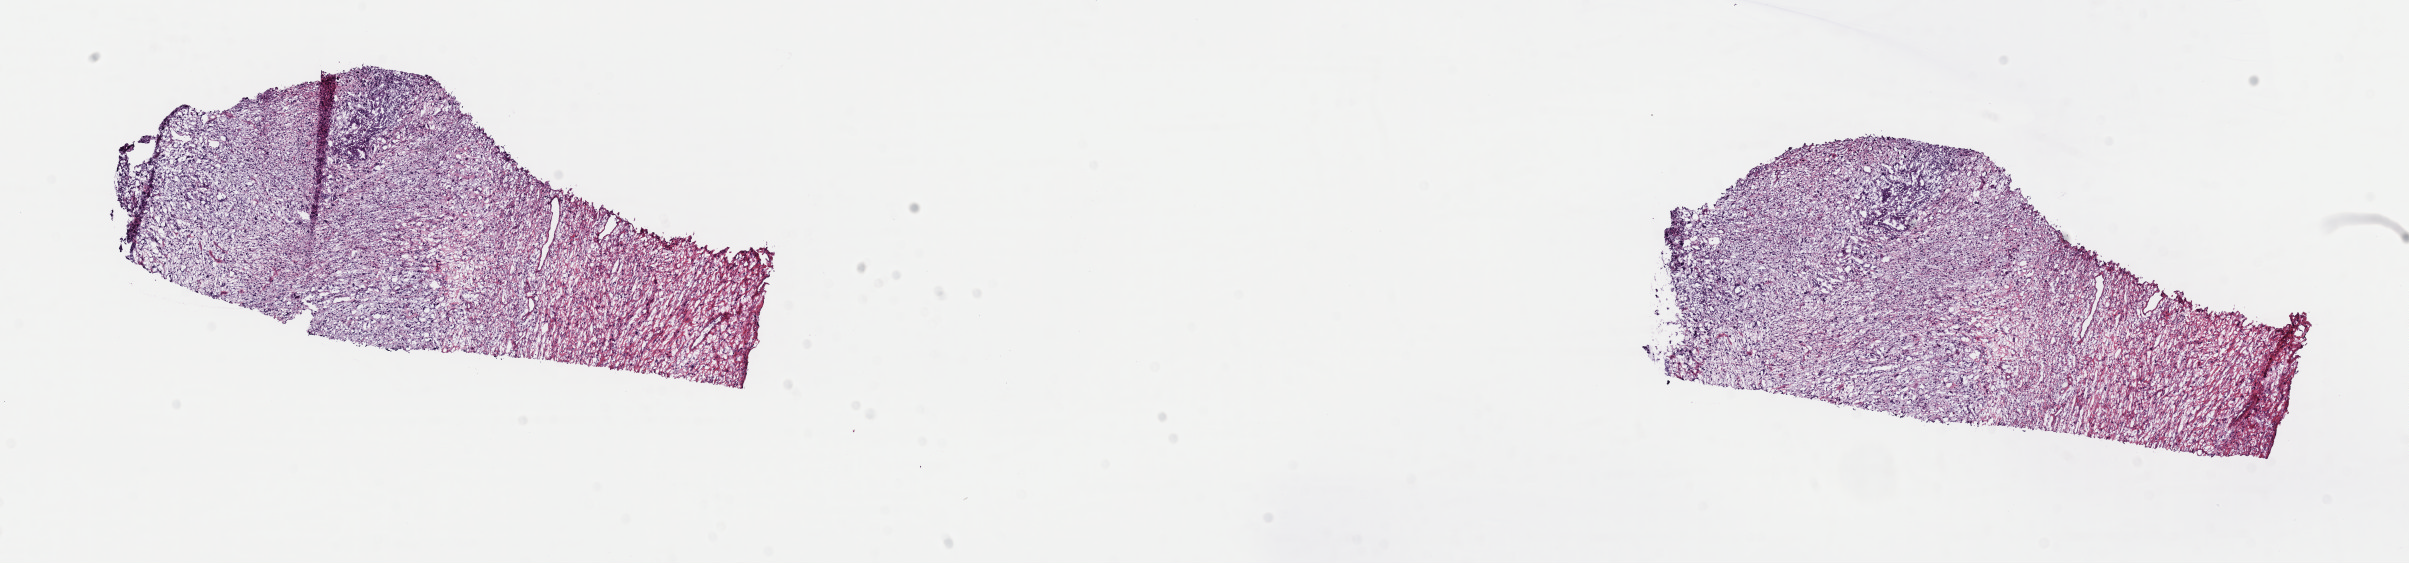
H&E whole-slide image — low-resolution overview of the scanned area, about 19.0 x 4.4 mm (acquisition: 40x scan), frozen section, uterus, primary tumour sample. Patient: female, age at initial diagnosis 72 years. Pathologist review of this section (percent, as recorded): tumour cells 100%, tumour nuclei 80%, normal cells 0%, stromal cells 0%, necrosis 0%. Infiltration values recorded for this section: lymphocyte infiltration 2%, monocyte infiltration 0%, neutrophil infiltration 0%.
FIGO stage: IB. Diagnosis: Basal cell carcinoma, NOS (corpus uteri).